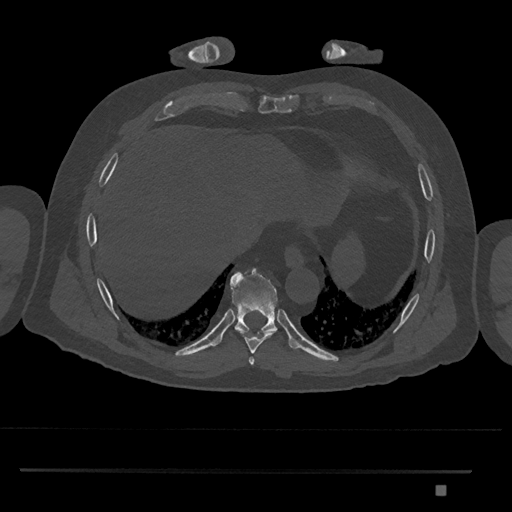
CT including the spine, one axial slice. Reconstruction kernel Br40s/3. Bone window (W 1800 / L 400 HU). 0.5 mm slice thickness. 512 × 512 image matrix, field of view 429 × 429 mm. Patient: male, 65 years. From the clinical record (not read from this slice): primary cancer: prostate.
Structures marked on this image (semi-automatic segmentation, software-assisted and operator-edited):
- T8 vertebra: bounding box (x1, y1, x2, y2) in pixels: (235, 329, 276, 355)
- T9 vertebra: (230, 268, 278, 334)